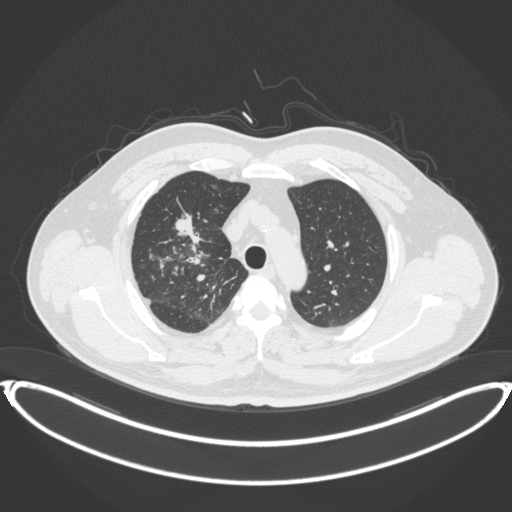
Chest CT, one axial slice; position 298 of 399 along the scan axis; 120 kVp; lung window (W 1500 / L -600 HU); 1 mm slice thickness; 512 × 512 image matrix, field of view 445 × 445 mm. Patient: male, 53 years. Case-level facts recorded for this patient, not image findings: clinical TNM (as recorded): T2a N0 M0.
Structures marked on this image (rectangle marked by the reading radiologist):
- lung tumour (recorded histology: adenocarcinoma): bounding box [x1, y1, x2, y2] px = [170, 205, 208, 248]